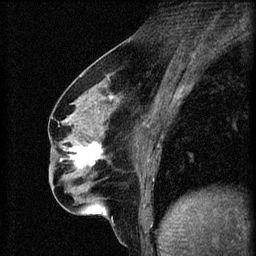
Breast MRI (dynamic contrast-enhanced), one sagittal slice; position 27 of 60 along the scan axis; 3 images stored at this slice position (order not interpretable as contrast timing); 1.5 T; TE 4.2 ms, TR 8.2 ms; 2 mm slice thickness; 256 × 256 image matrix, field of view 180 × 180 mm. Female patient, age 56 years.
Outlined on this slice (semi-automatically segmented with operator editing):
- analysis volume of interest (the breast-tissue region the enhancement analysis was run in; not a lesion): bounding box <62,136,111,179> (left, top, right, bottom; pixels)
- tumour enhancement mask (voxels above the 70 % enhancement threshold inside the analysis volume of interest): <69,142,103,169>